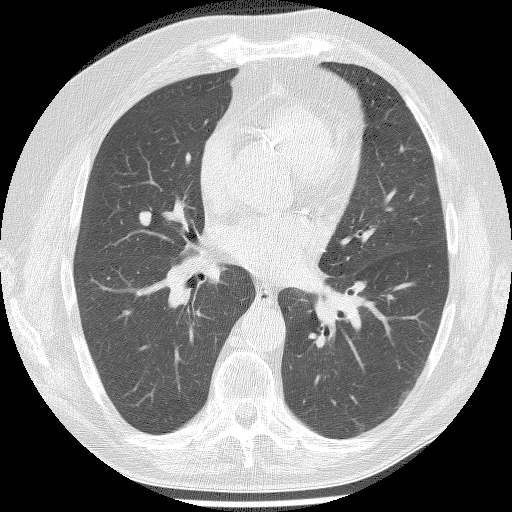
Low-dose screening chest CT, axial slice. Second screening round (one year after baseline). Lung window (W 1500 / L -600 HU). 120 kVp. Male, age 61 years at enrolment. Current smoker at enrolment.
- Lesion marked by an expert reader, bounding box [x1, y1, x2, y2] px = [122, 199, 158, 238].
- The screening reader recorded 2 non-calcified nodules or masses ≥4 mm on this exam; which of them this box marks is not recorded.
- Participant outcome: lung cancer diagnosed 147 days after this screen — bronchiolo-alveolar adenocarcinoma, NOS, right middle lobe, well differentiated (G1), stage IA (AJCC 6th edition), 15 mm at pathology.